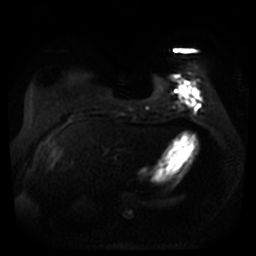
Breast MRI, one axial slice; slice 9 of 44 in the series (ordered by position); diffusion-weighted series; image 2 of 4 stored at this slice position (different b-values; order by instance number); 3 T; 5 mm slice thickness; 256 × 256 image matrix, field of view 360 × 360 mm. Female patient.
Structures marked on this image (manually delineated by an expert):
- tumour on diffusion-weighted imaging: bounding box [x1, y1, x2, y2] px = [178, 83, 198, 103]